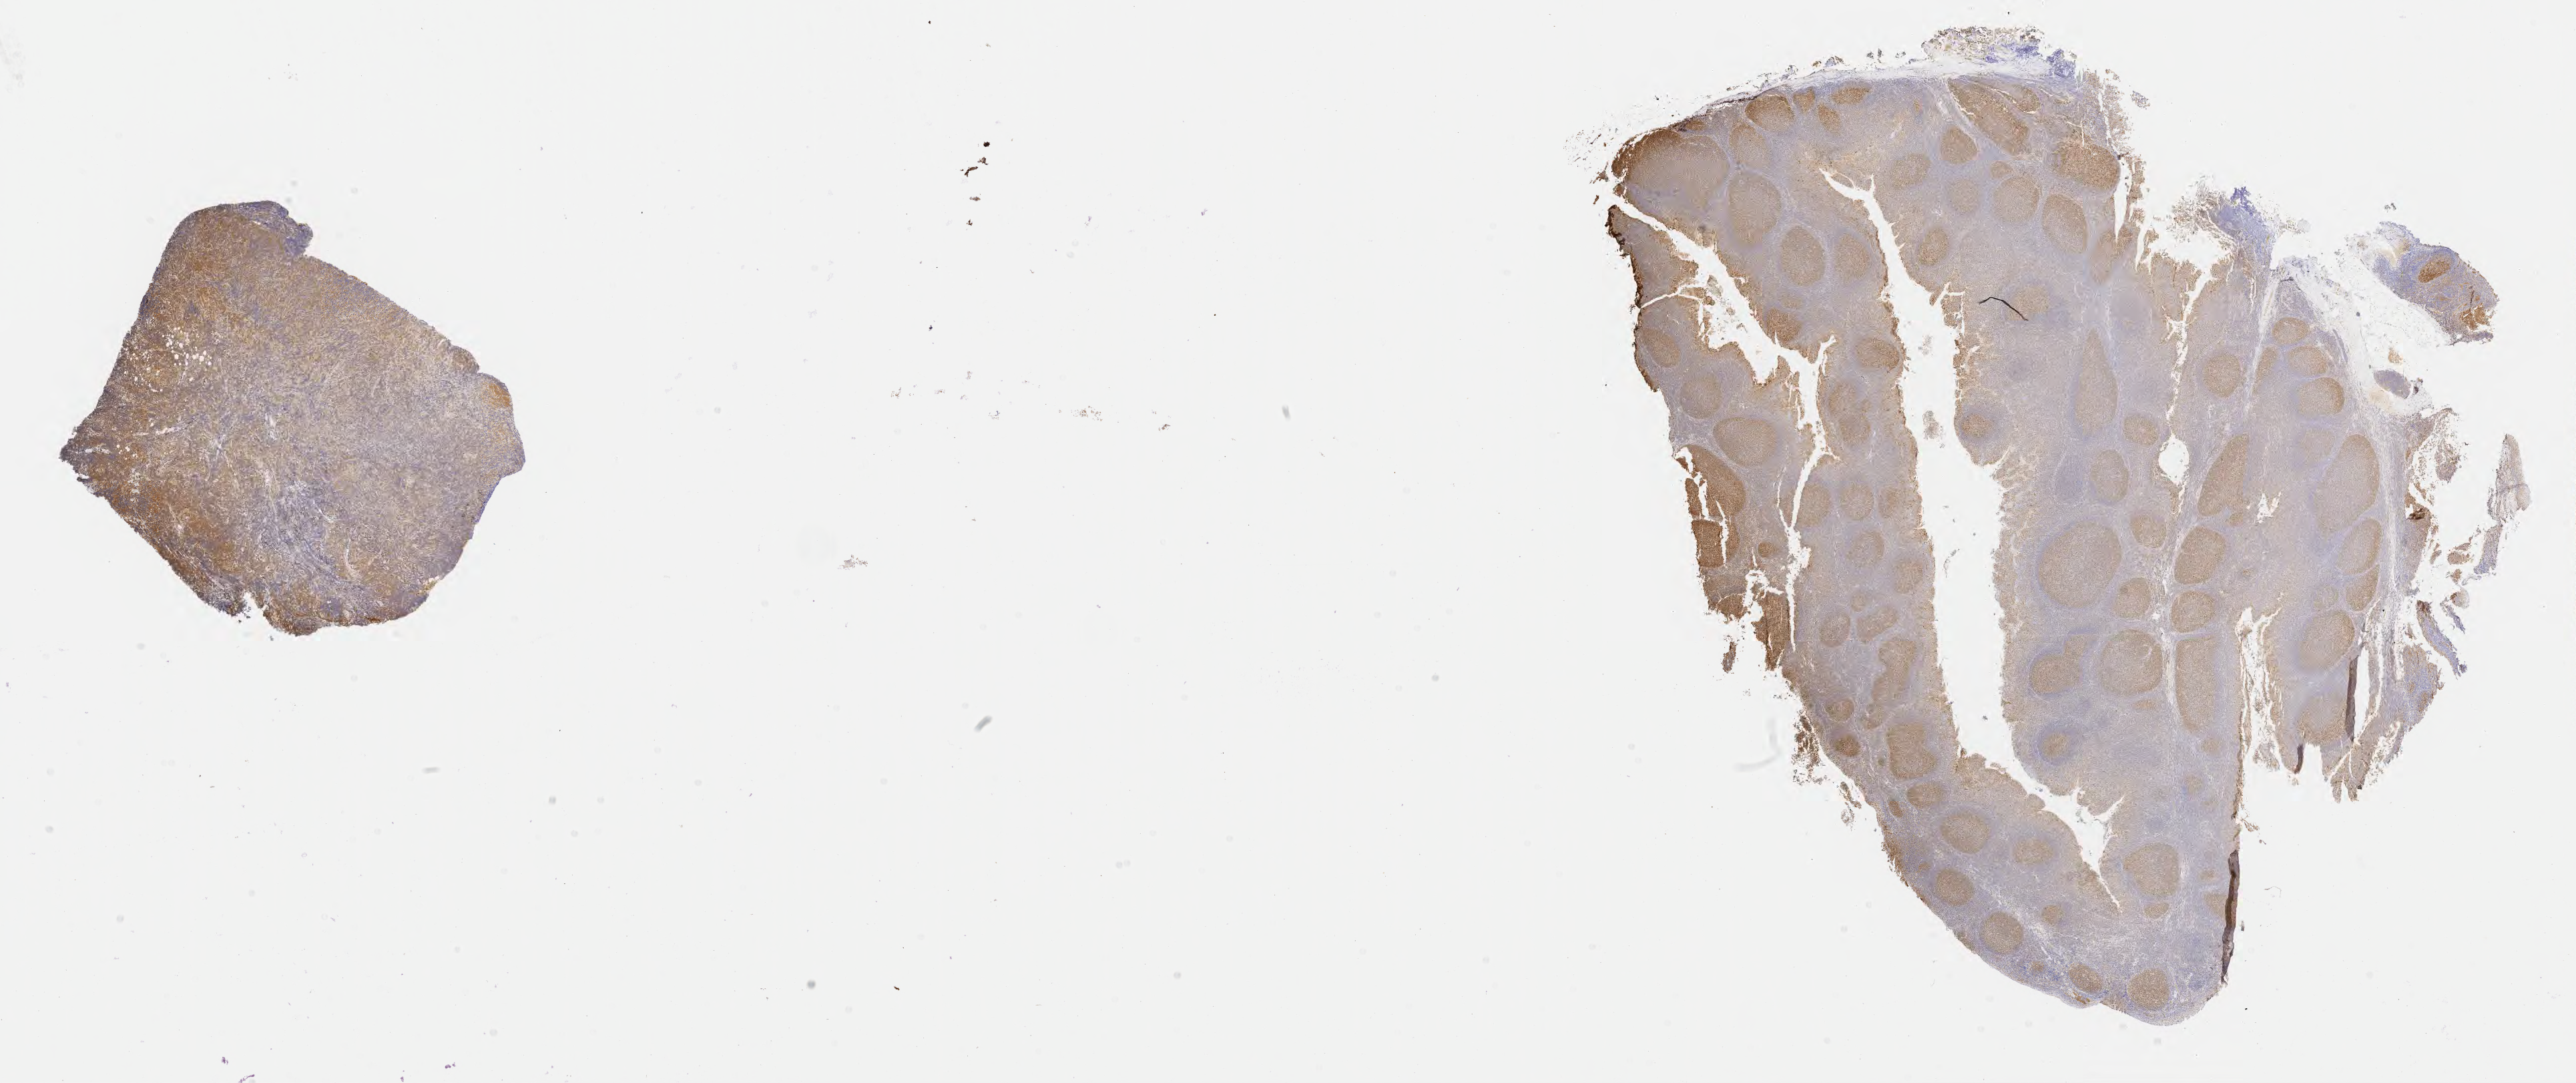
Whole-slide image, immunohistochemical stain for BCL6 — low-resolution overview of the scanned area, about 31.2 x 13.1 mm, tumor tissue, anatomic site: buccal mucosa. Male, age 7 years at initial diagnosis.
Histologic diagnosis: Burkitt lymphoma, NOS.